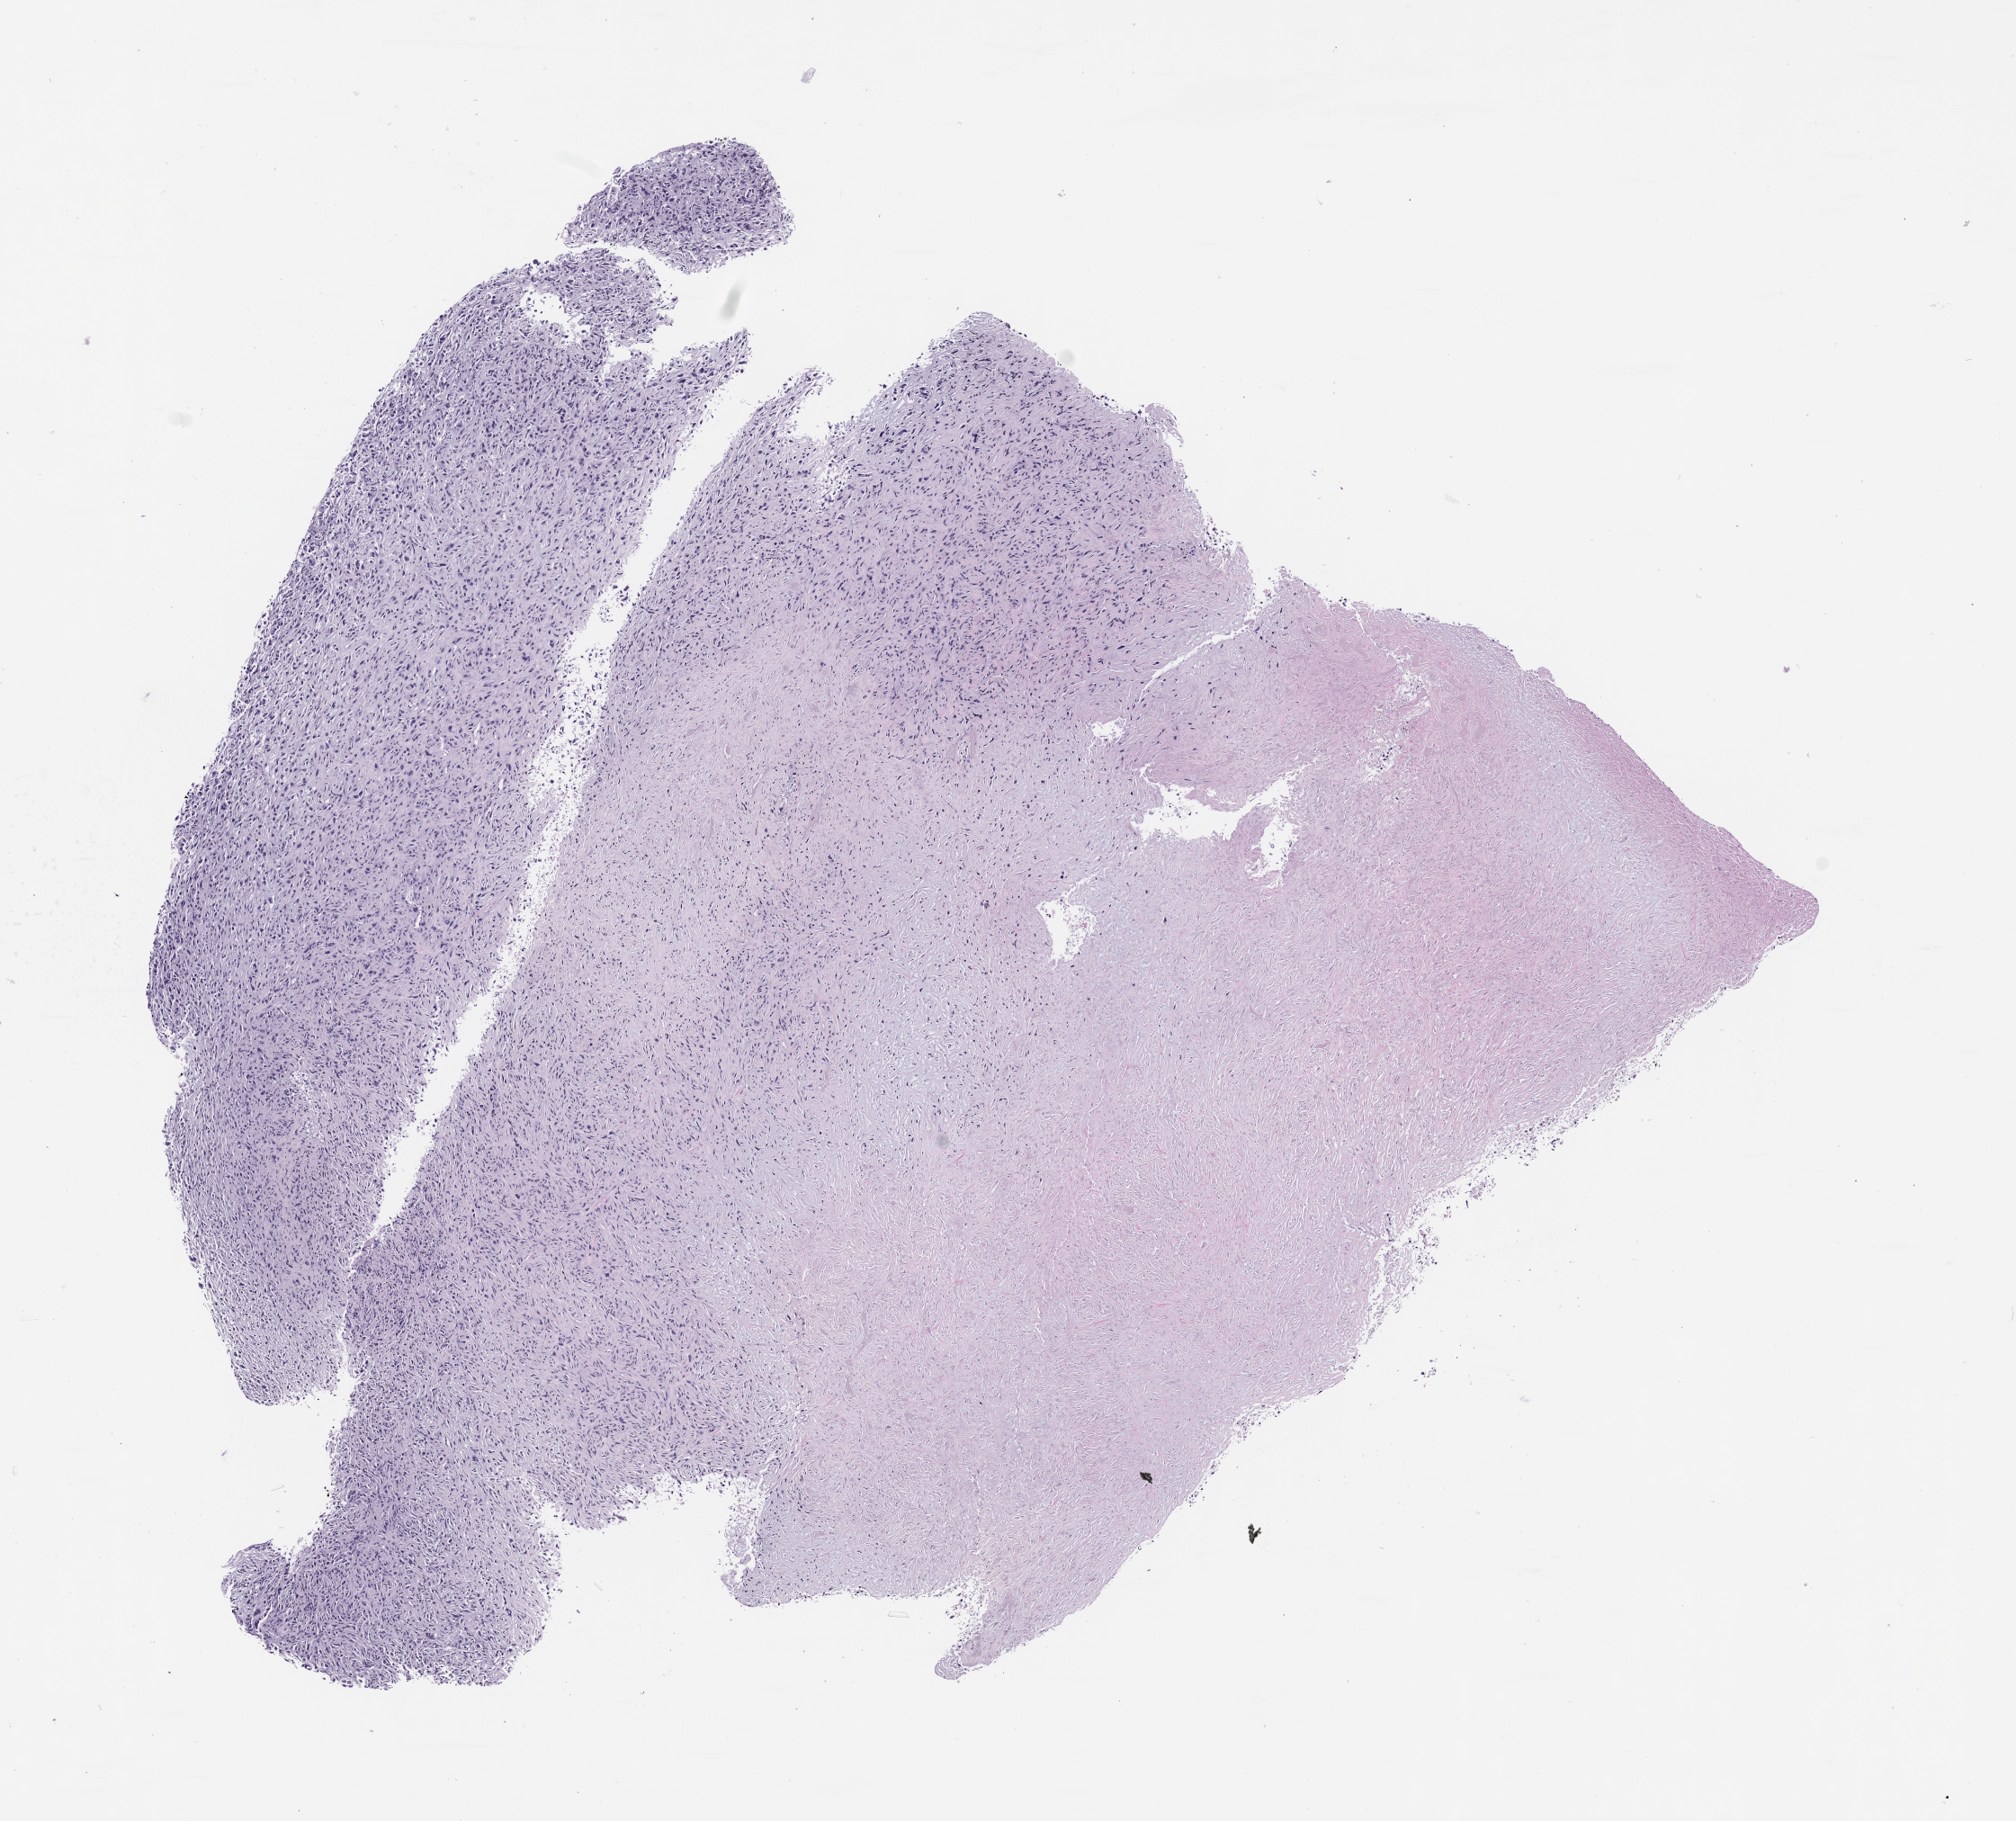
Whole-slide image, haematoxylin and eosin: patient-derived xenograft (human tumor grown in a mouse) — whole scanned area (about 9.0 x 8.1 mm) shown as a low-resolution overview. FFPE section. Originating tumor site category: musculoskeletal.
Originating patient diagnosis: Spindle Cell Sarcoma.